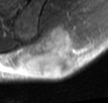
MRI of an extremity soft-tissue mass, one axial slice. Position 18 of 42 along the scan axis. T2-weighted fat-saturated. MR volume resampled by the dataset authors to the PET/CT grid (not the native acquisition matrix). 3.27 mm slice thickness. 108 × 103 image matrix. Male patient. From the clinical record (not read from this slice): histological type: leiomyosarcoma; grade: intermediate; site of the primary tumour: left pelvis.
Annotated regions visible in this slice (expert contour drawn on MRI and transferred to this co-registered scan by the dataset authors):
- gross tumour volume (mass): bounding box <23,24,79,77> (left, top, right, bottom; pixels)